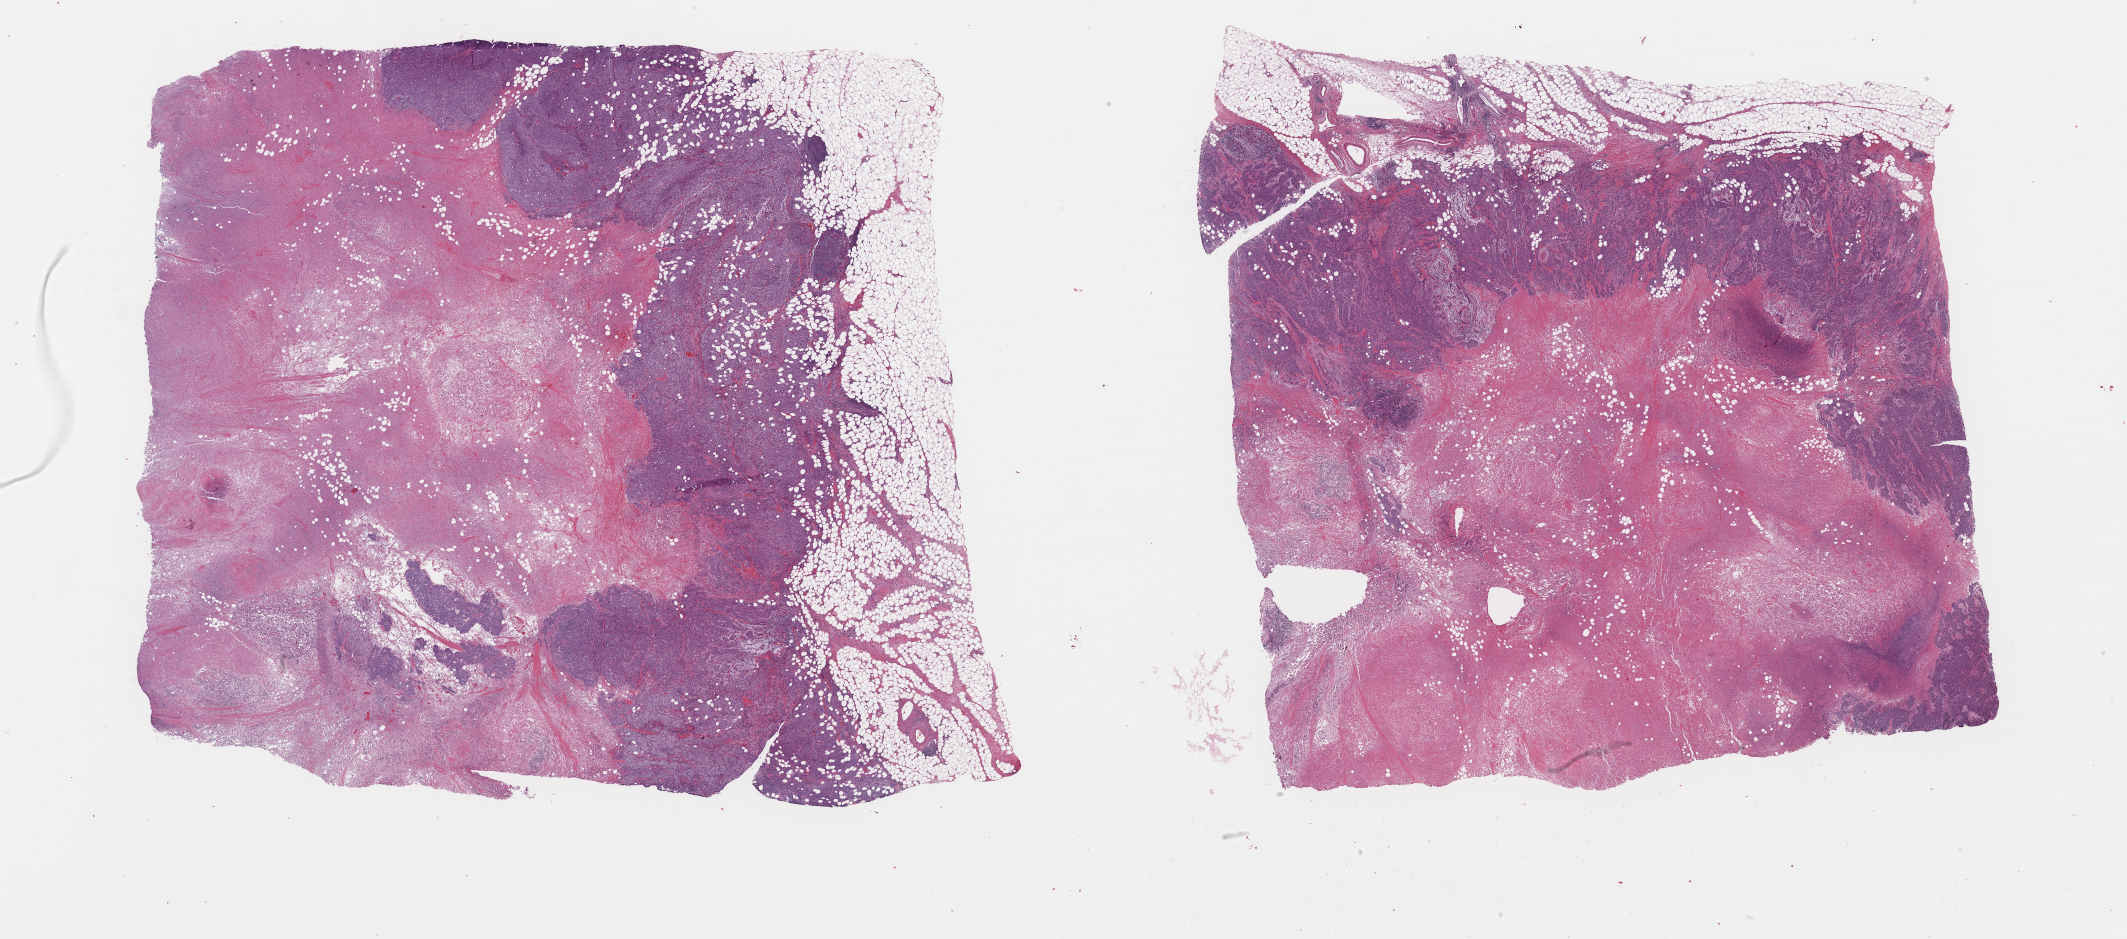
H&E-stained whole-slide image, low-resolution overview of the scanned area, about 33.6 x 14.8 mm (acquisition: 40x scan); FFPE section; primary tumour sample from the breast. Female patient; age at initial diagnosis 35 years.
• lymph nodes positive (case pathology): 0 of 4 examined
• laterality: right
• AJCC pathologic stage: IIA (6th edition)
• diagnosis: Infiltrating duct carcinoma, NOS